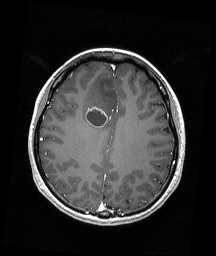
Brain MRI from a brain-tumour surgery series, one axial slice. Position 68 of 192 along the scan axis. T1-weighted post-contrast. 1 mm slice thickness. 216 × 256 image matrix, field of view 211 × 250 mm. Case-level facts recorded for this patient, not image findings: histopathology: Astrocytoma; WHO grade: 4; IDH mutation: yes; tumour location: Right Frontal.
Outlined on this slice (manually delineated by an expert):
- tumour: bounding box [x1, y1, x2, y2] px = [85, 106, 108, 127]